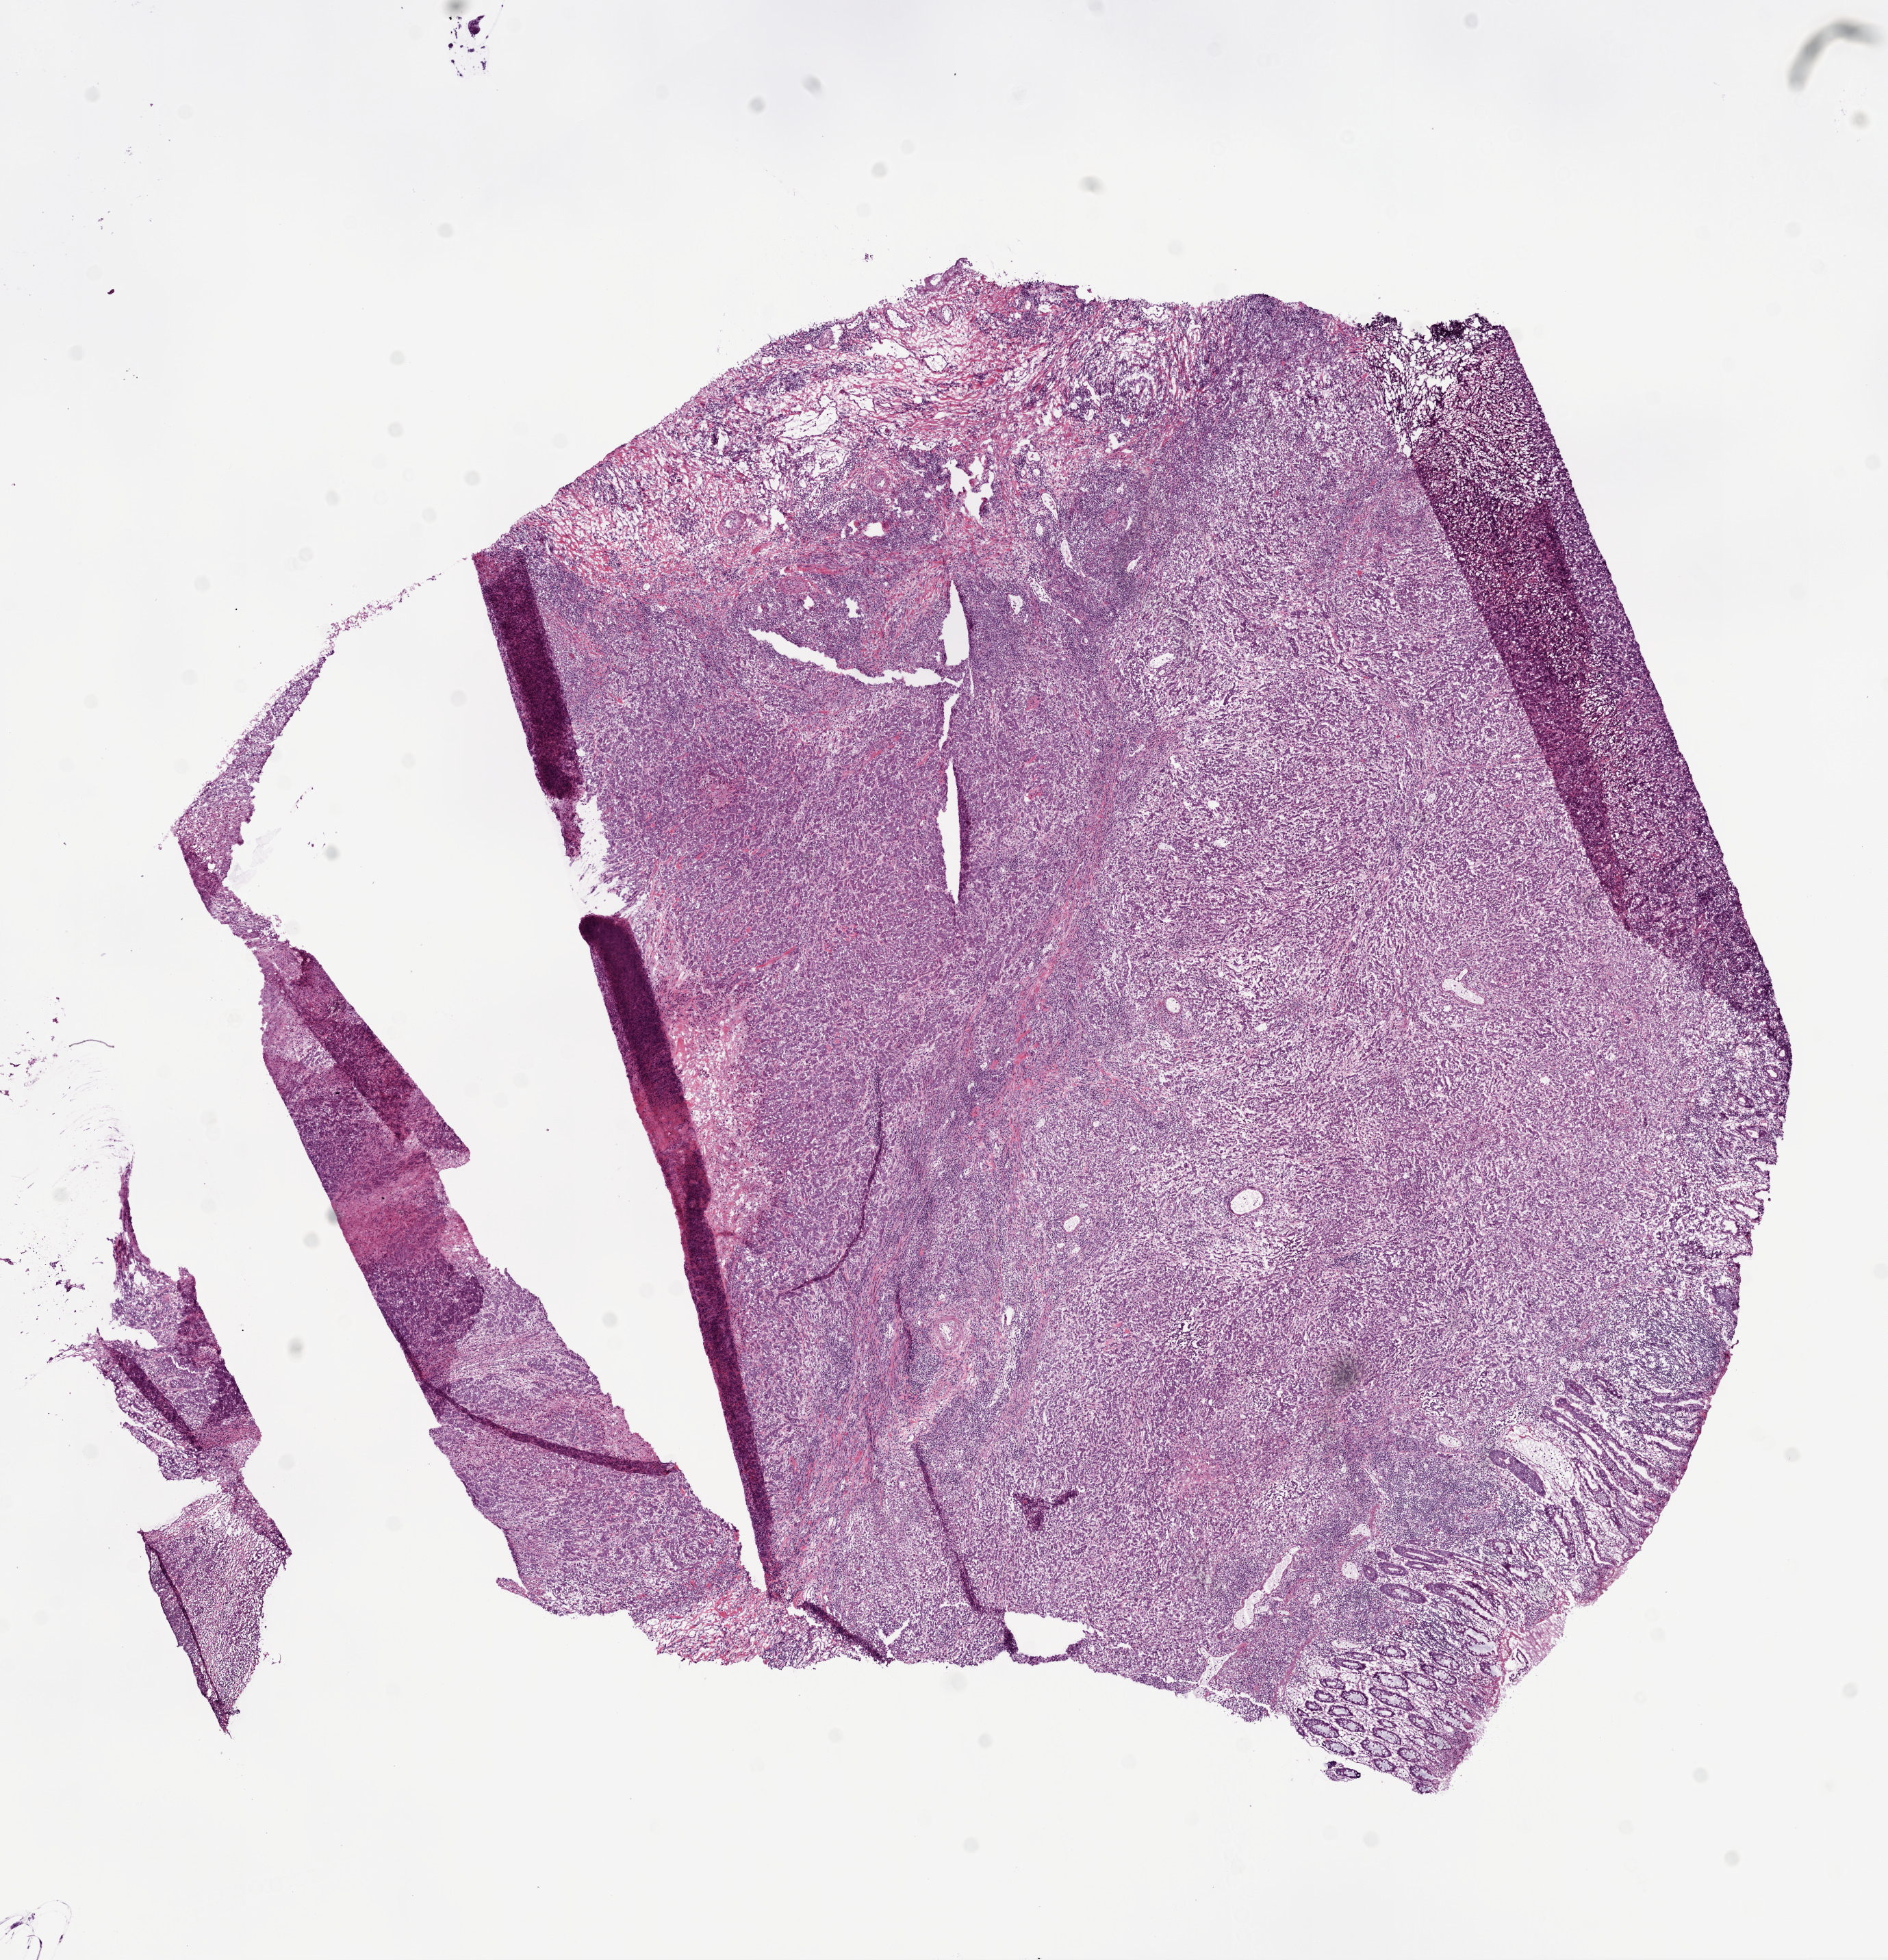
H&E-stained whole-slide image, shown as a low-resolution overview of the whole scanned area (about 11.1 x 11.5 mm, acquisition: 20x scan). Frozen section from the bottom of the tissue portion. Primary tumour sample from the colon. Patient: female, age at initial diagnosis 68 years. Pathologist review of this section (percent, as recorded): tumour cells 67%, tumour nuclei 75%, normal cells 8%, stromal cells 10%, necrosis 15%.
• diagnosis: Adenocarcinoma, NOS (sigmoid colon)
• AJCC pathologic stage: IIA (7th edition)